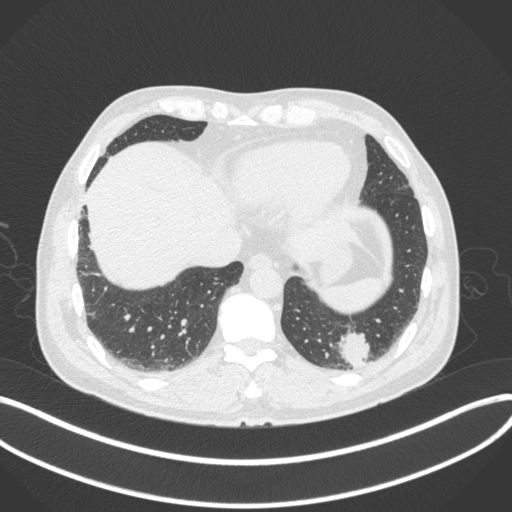
Chest CT, one axial slice; position 61 of 313 along the scan axis; lung window (W 1500 / L -600 HU); 1 mm slice thickness; 512 × 512 image matrix, field of view 400 × 400 mm. Male patient, age 54 years. Case-level facts recorded for this patient, not image findings: clinical TNM (as recorded): T1c N0 M1.
Outlined on this slice (rectangle marked by the reading radiologist):
- lung tumour (recorded histology: adenocarcinoma): bounding box (x1, y1, x2, y2) in pixels: (333, 328, 378, 368)